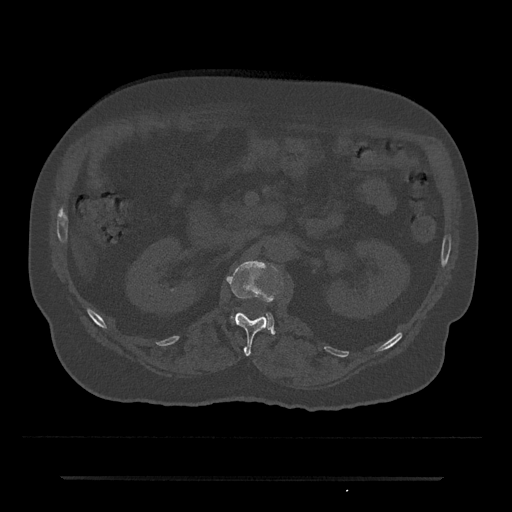
CT including the spine, one axial slice; slice 53 of 797 in the series (ordered by position); reconstruction kernel Br40s/3; 120 kVp; bone window (W 1800 / L 400 HU); 512 × 512 image matrix, field of view 437 × 437 mm. Male patient, age 69 years. From the clinical record (not read from this slice): primary cancer: prostate.
Outlined on this slice (semi-automatic segmentation, software-assisted and operator-edited):
- L1 vertebra: bounding box (x1, y1, x2, y2) in pixels: (227, 260, 283, 356)
- L2 vertebra: (231, 313, 275, 334)